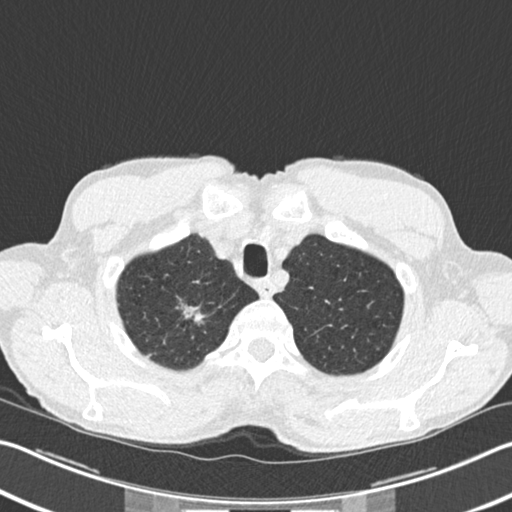
Low-dose screening chest CT, one axial slice. Position 194 of 220 along the scan axis. Reconstruction kernel B30f. 120 kVp. Lung window (W 1500 / L -600 HU). 2 mm slice thickness. 512 × 512 image matrix, field of view 342 × 342 mm.
Structures marked on this image (expert manual segmentation):
- lesion 1 (tumor, upper lobe of right lung): bounding box <181,304,204,324> (left, top, right, bottom; pixels)